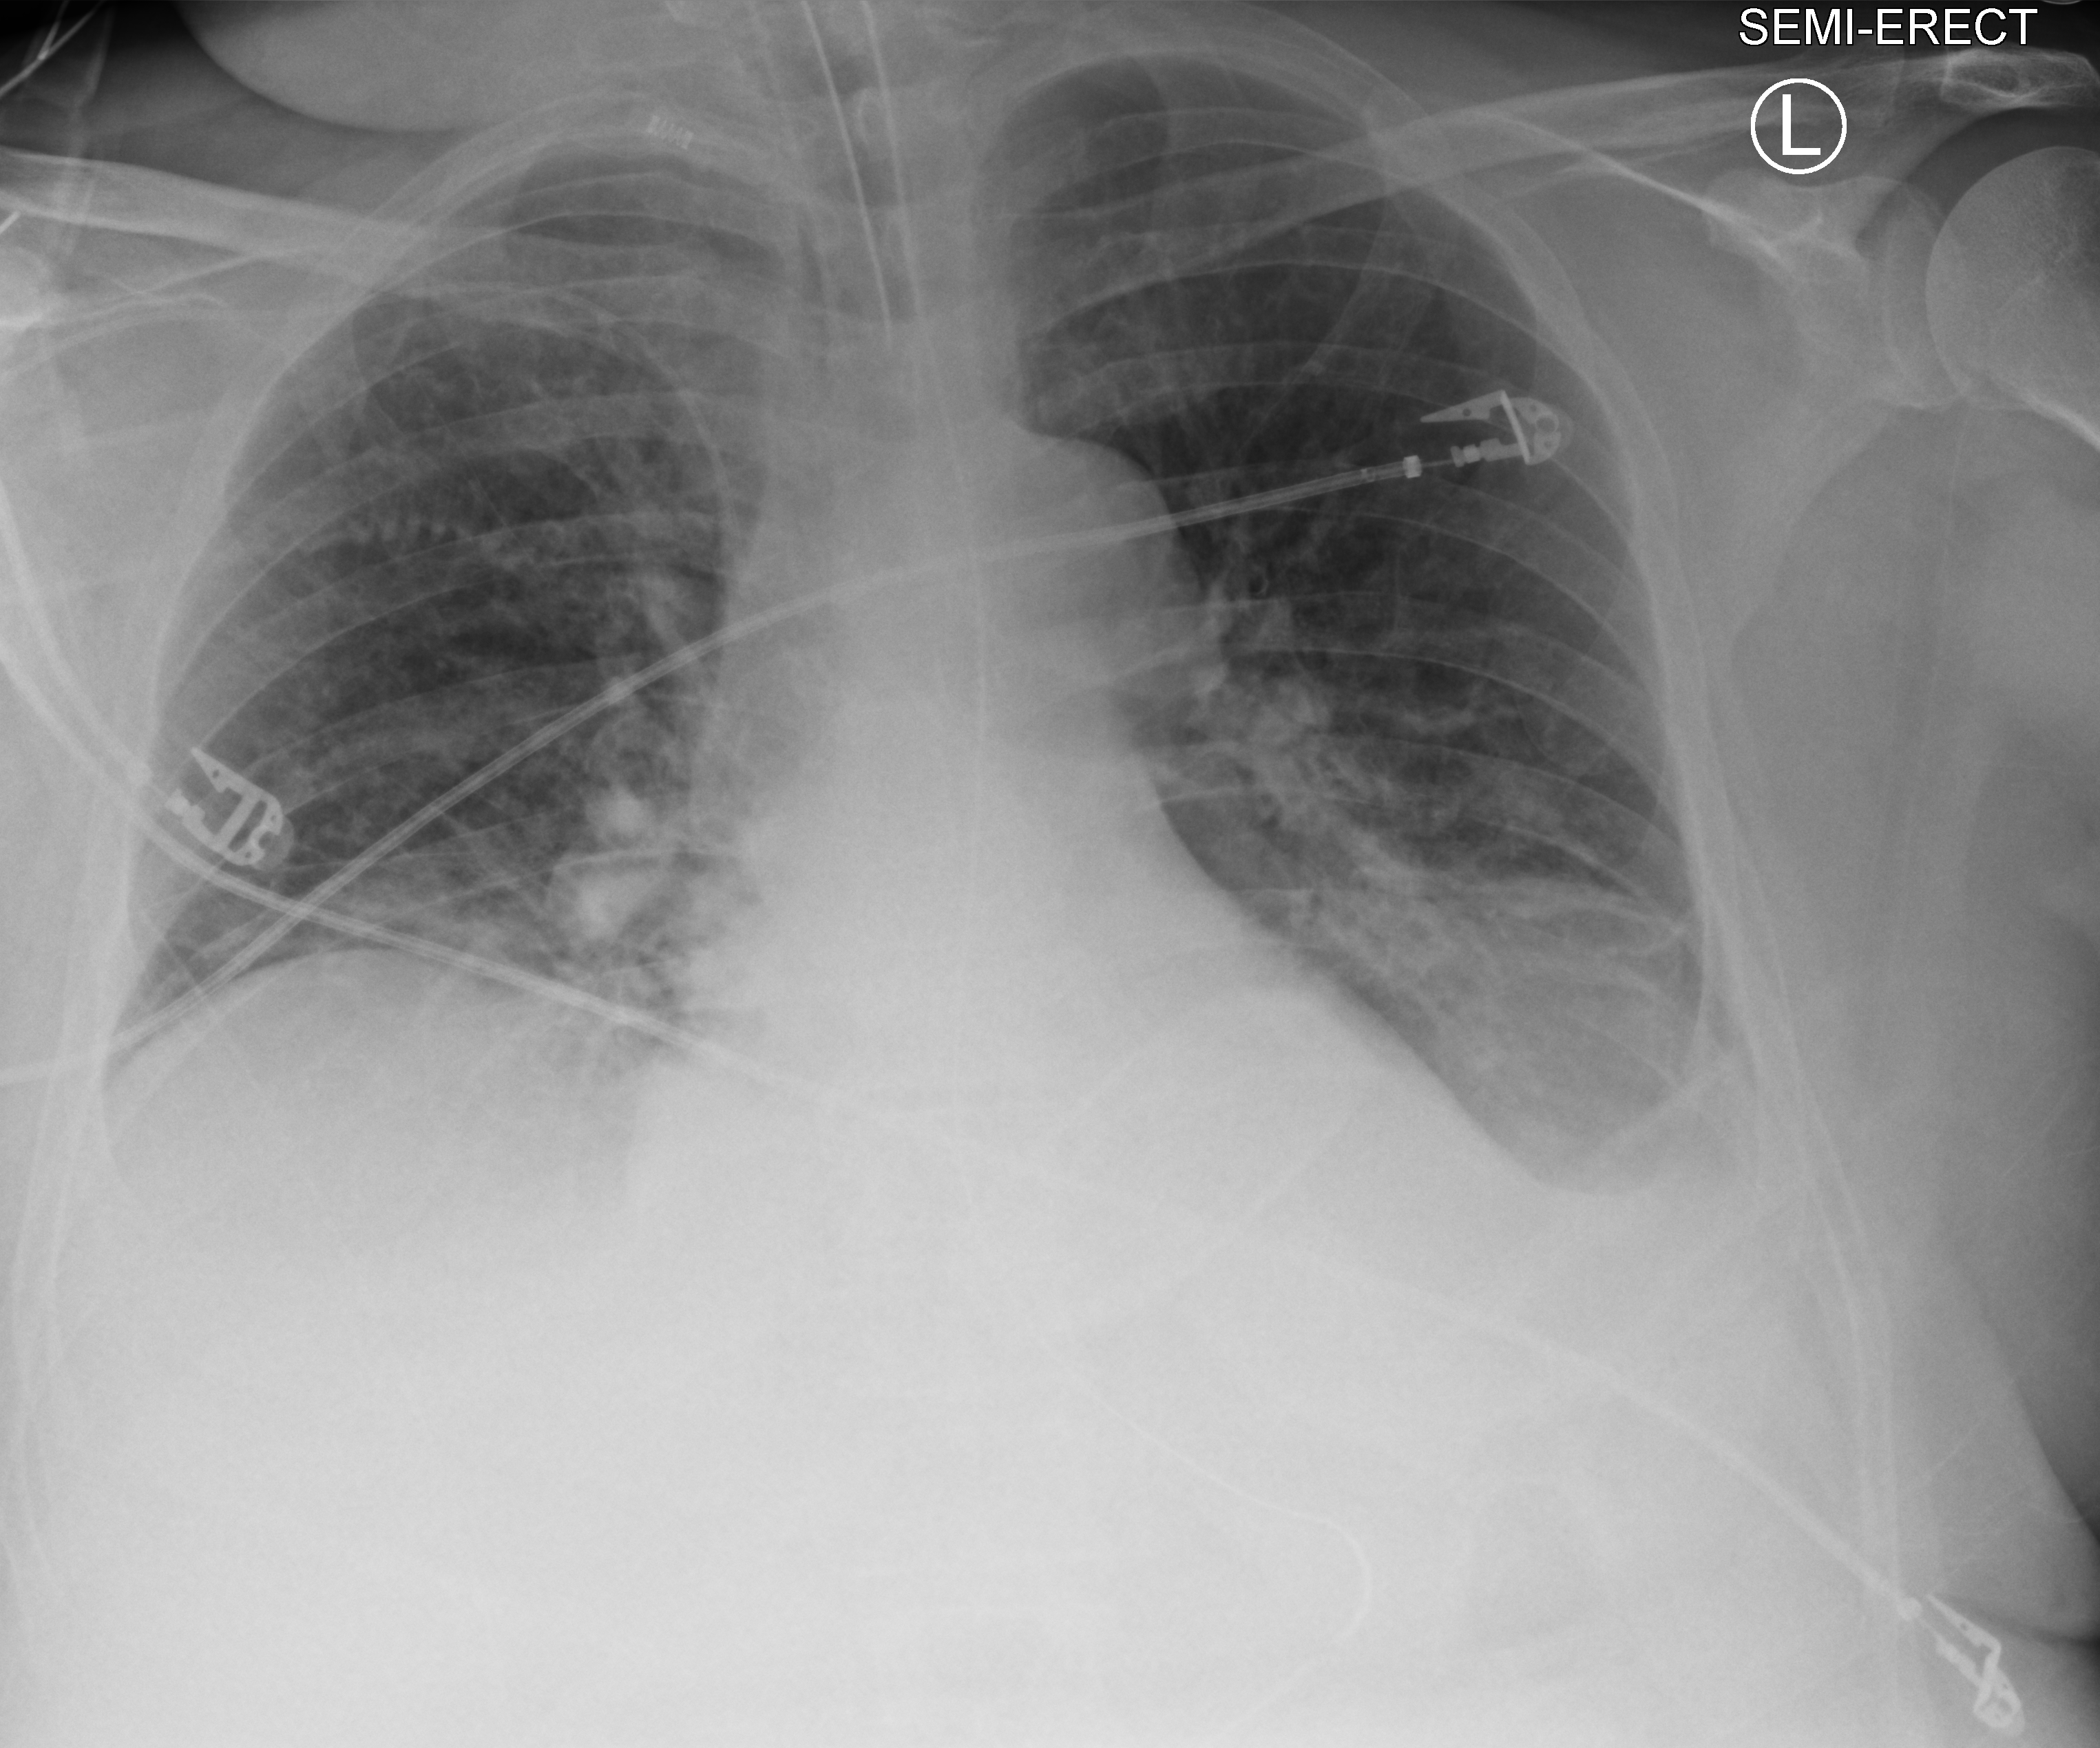
Bedside chest radiograph (computed radiography), anteroposterior (AP) projection. Patient hospitalised with COVID-19; male, aged 60–74 years.
From the hospital-stay record, not from the radiograph (when in the stay this image was taken is not recorded):
- hypertension (admission record): no